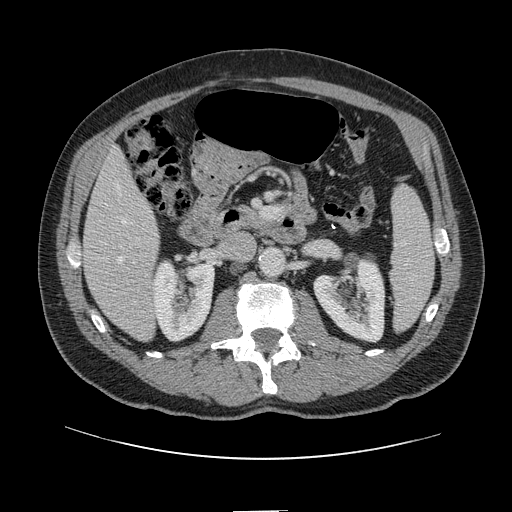
Contrast-enhanced abdominal CT, one axial slice. Position 44 of 161 along the scan axis. 120 kVp. Intravenous contrast given. Soft-tissue window (W 400 / L 40 HU). 512 × 512 image matrix, field of view 412 × 412 mm. Male patient, age 66 years. From the clinical record (not read from this slice): diagnosis: colorectal cancer liver metastases, imaged before liver resection.
Structures marked on this image (outlined manually by an expert reader):
- hepatic veins: box from (x=119, y=220) to (x=126, y=262) px
- liver: (x=84, y=152)–(x=158, y=341)
- planned liver remnant (the part of the liver to remain after resection): (x=83, y=152)–(x=155, y=273)